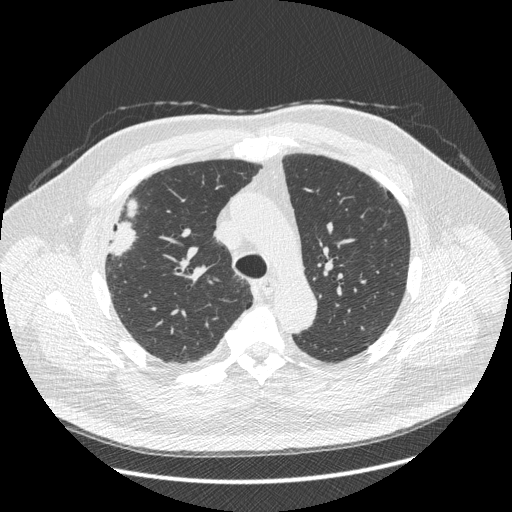
Low-dose screening chest CT, one axial slice; reconstruction kernel STANDARD; 120 kVp; lung window (W 1500 / L -600 HU); 1.25 mm slice thickness; 512 × 512 image matrix, field of view 400 × 400 mm.
Annotated regions visible in this slice (outlined manually by an expert reader):
- lesion 1 (tumor, upper lobe of right lung): bounding box (x1, y1, x2, y2) in pixels: (109, 200, 137, 255)